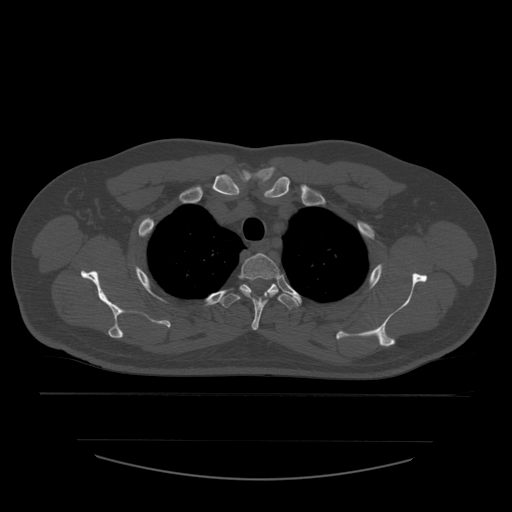
CT including the spine, one axial slice; position 443 of 532 along the scan axis; reconstruction kernel STANDARD; bone window (W 1800 / L 400 HU); 512 × 512 image matrix. Patient age 44 years. Case-level facts recorded for this patient, not image findings: primary cancer: soft tissue sarcoma.
Annotated regions visible in this slice (semi-automatic segmentation, software-assisted and operator-edited):
- T2 vertebra: box from (x=239, y=253) to (x=281, y=331) px
- T3 vertebra: (x=218, y=279)–(x=299, y=309)